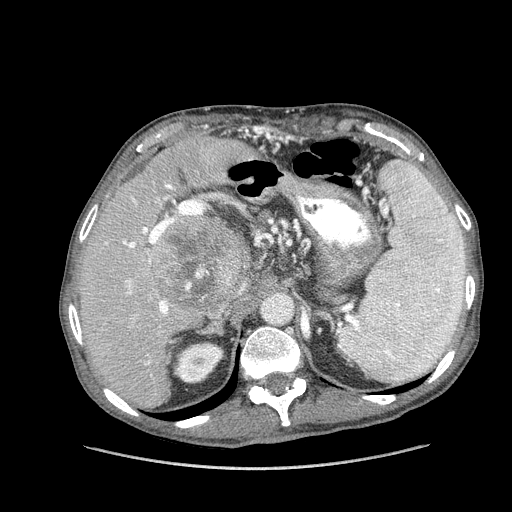
Contrast-enhanced abdominal CT (liver protocol), one axial slice; slice 93 of 162 in the series (ordered by position); reconstruction kernel STANDARD; soft-tissue window (W 400 / L 40 HU); 512 × 512 image matrix. Case-level facts recorded for this patient, not image findings: diagnosis: hepatocellular carcinoma (patient treated with transarterial chemoembolisation; whether this scan precedes or follows treatment is not stated here); TNM stage (as recorded): Stage-IIIA; Child-Pugh class: A; tumour nodularity: multinodular.
Structures marked on this image (semi-automatic segmentation, software-assisted and operator-edited):
- liver parenchyma outside the tumour (the mass and vessels are separate outlines, so this box may not span the whole liver): bounding box (x1, y1, x2, y2) in pixels: (78, 134, 256, 408)
- mass: (150, 211, 250, 312)
- liver vessels: (104, 184, 222, 365)